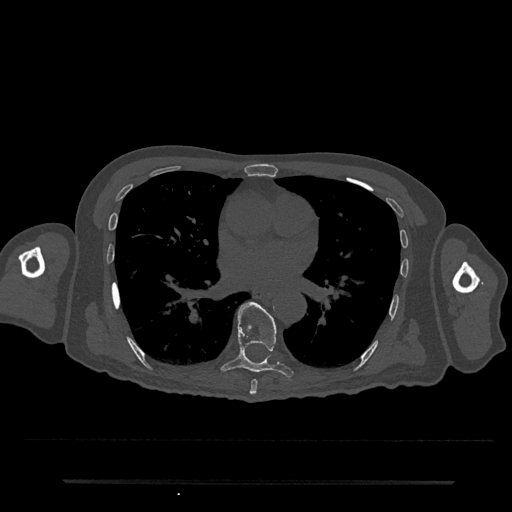
CT including the spine, one axial slice; position 430 of 797 along the scan axis; reconstruction kernel Br40s/3; 120 kVp; bone window (W 1800 / L 400 HU); 512 × 512 image matrix, field of view 427 × 427 mm. Male patient, age 74 years. Case-level facts recorded for this patient, not image findings: primary cancer: prostate.
Annotated regions visible in this slice (semi-automatically segmented with operator editing):
- T7 vertebra: bounding box <250,380,258,395> (left, top, right, bottom; pixels)
- T8 vertebra: <221,302,294,379>